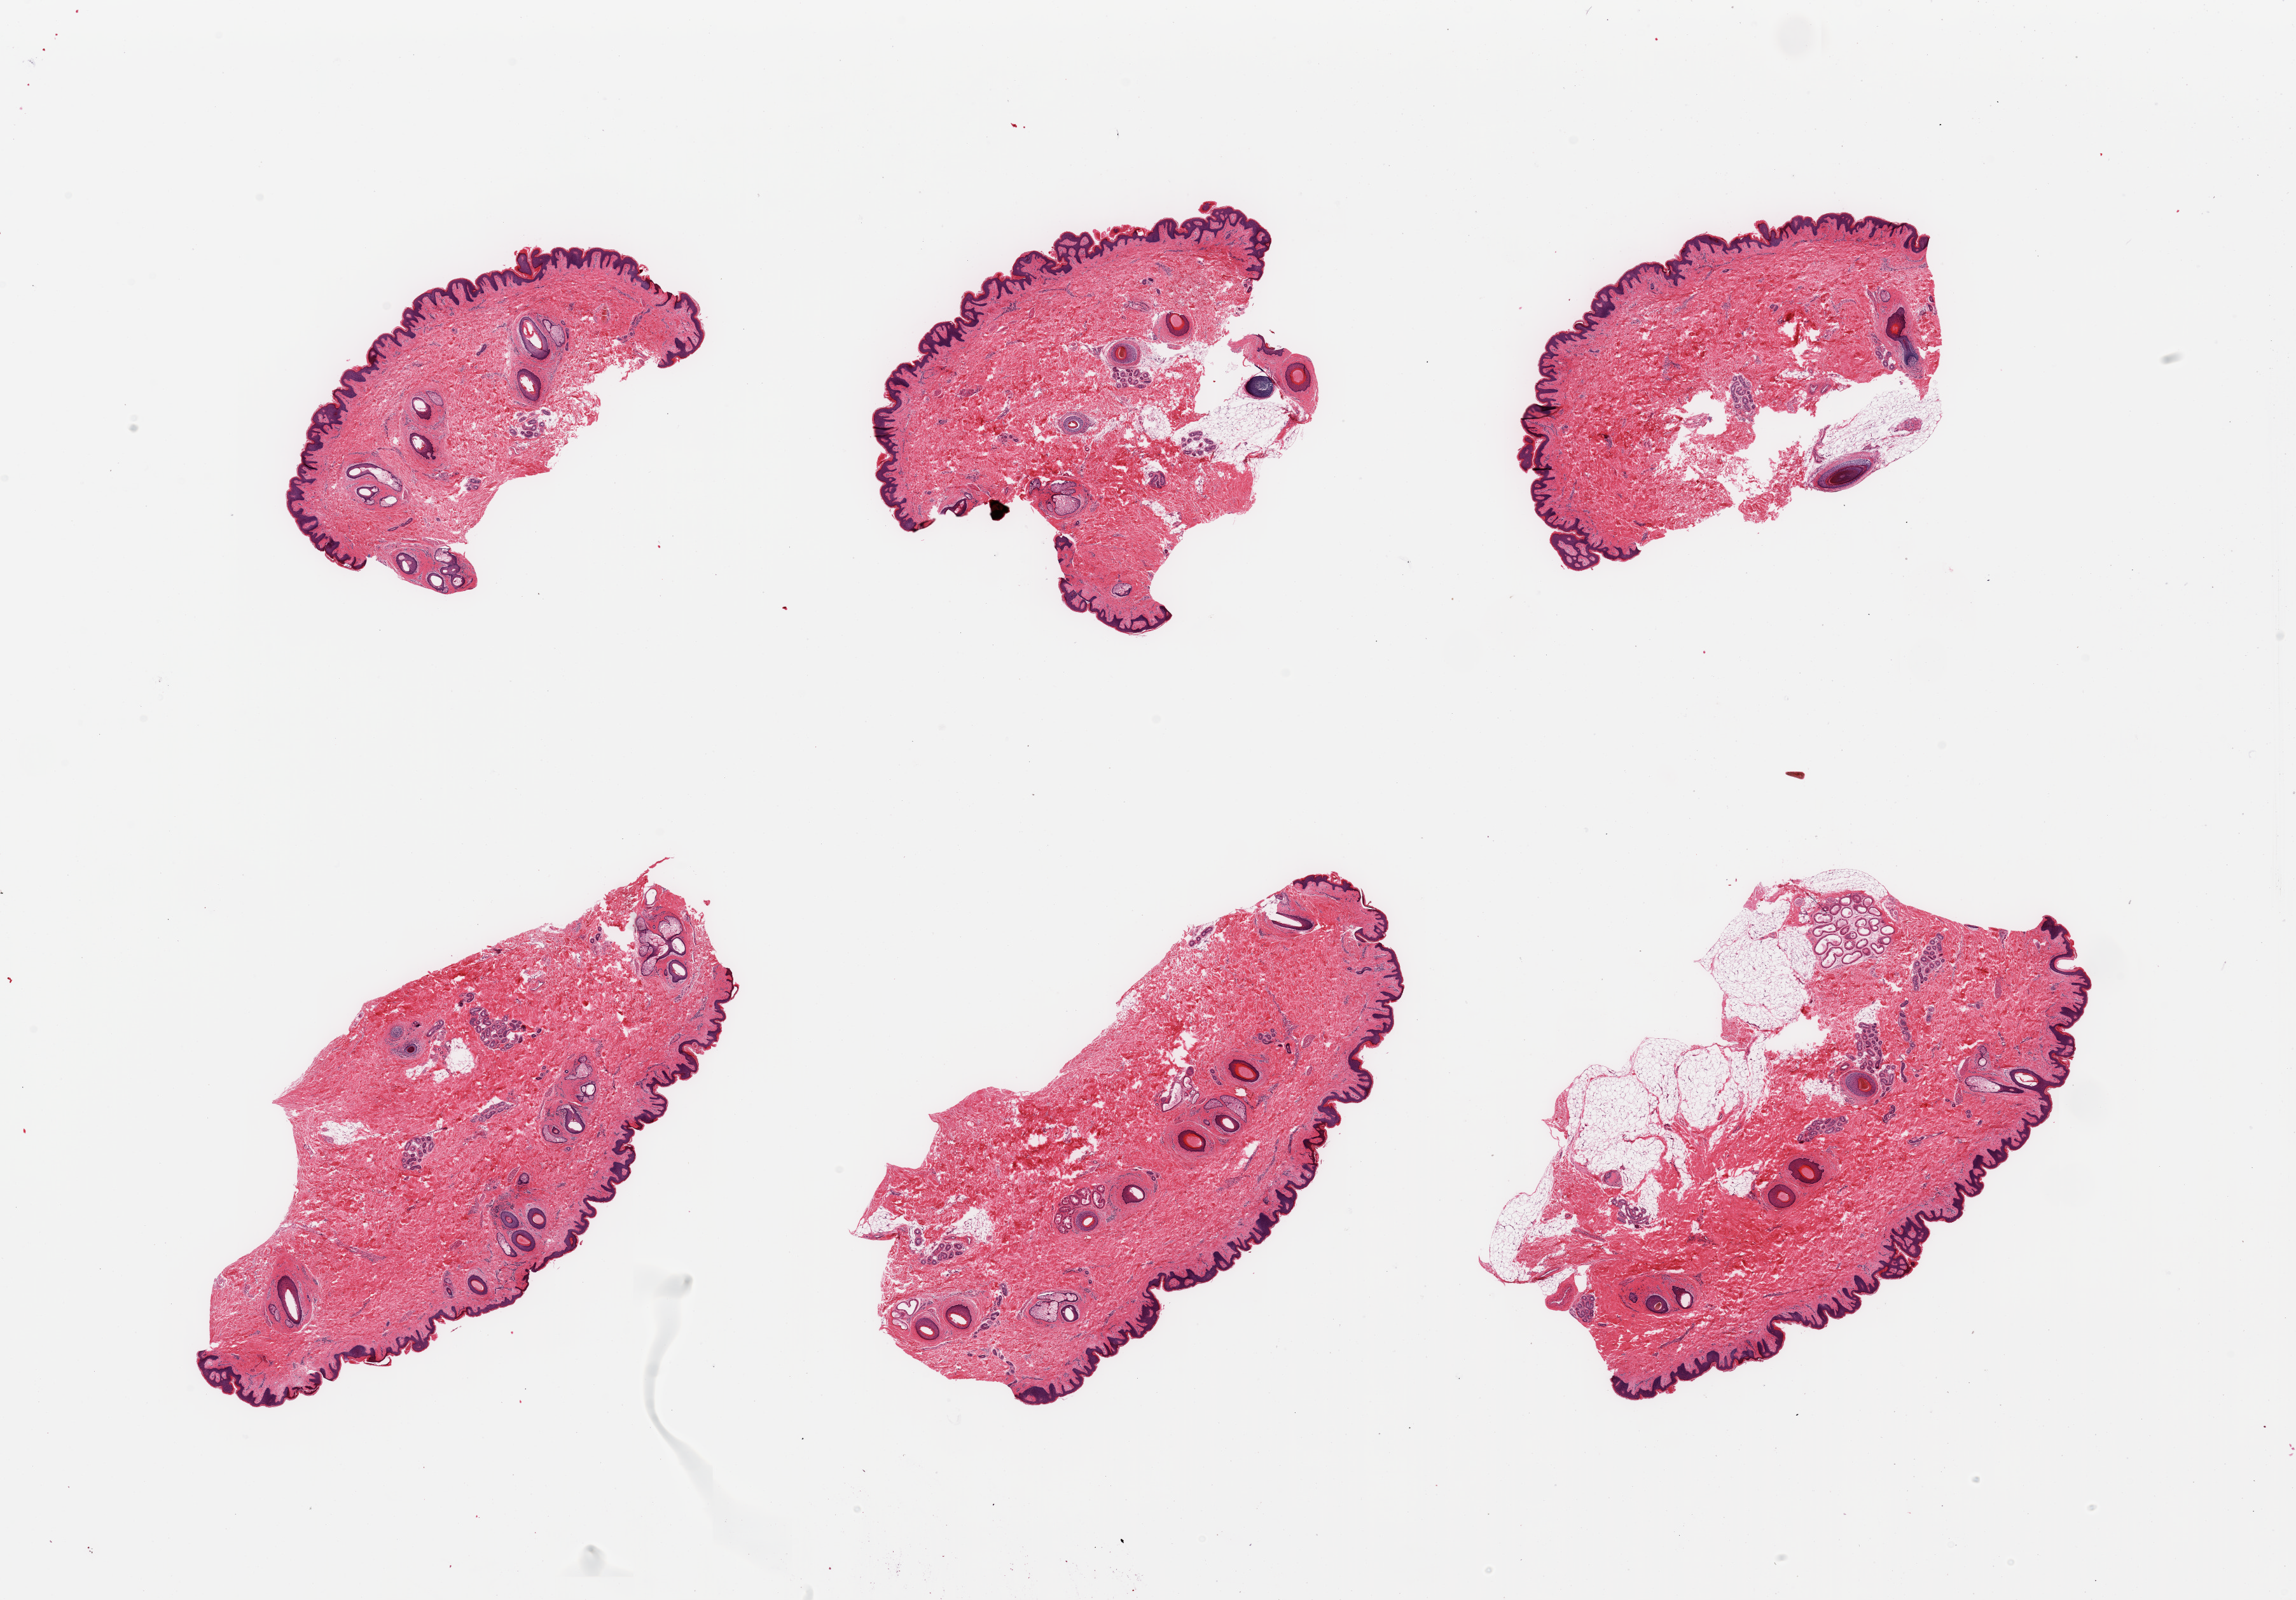
Digitized haematoxylin and eosin-stained section, brightfield — shown as a low-resolution overview of the whole scanned area (about 28.5 x 19.9 mm). PAXgene-fixed, paraffin-embedded tissue. Sampled site (target tissue): skin of suprapubic region. Tissue donor sample.
Pathologist's review note for this sample: 6 pieces; up to 8 hair follicles per piece; subcutaneous fat up to 1mm thick.